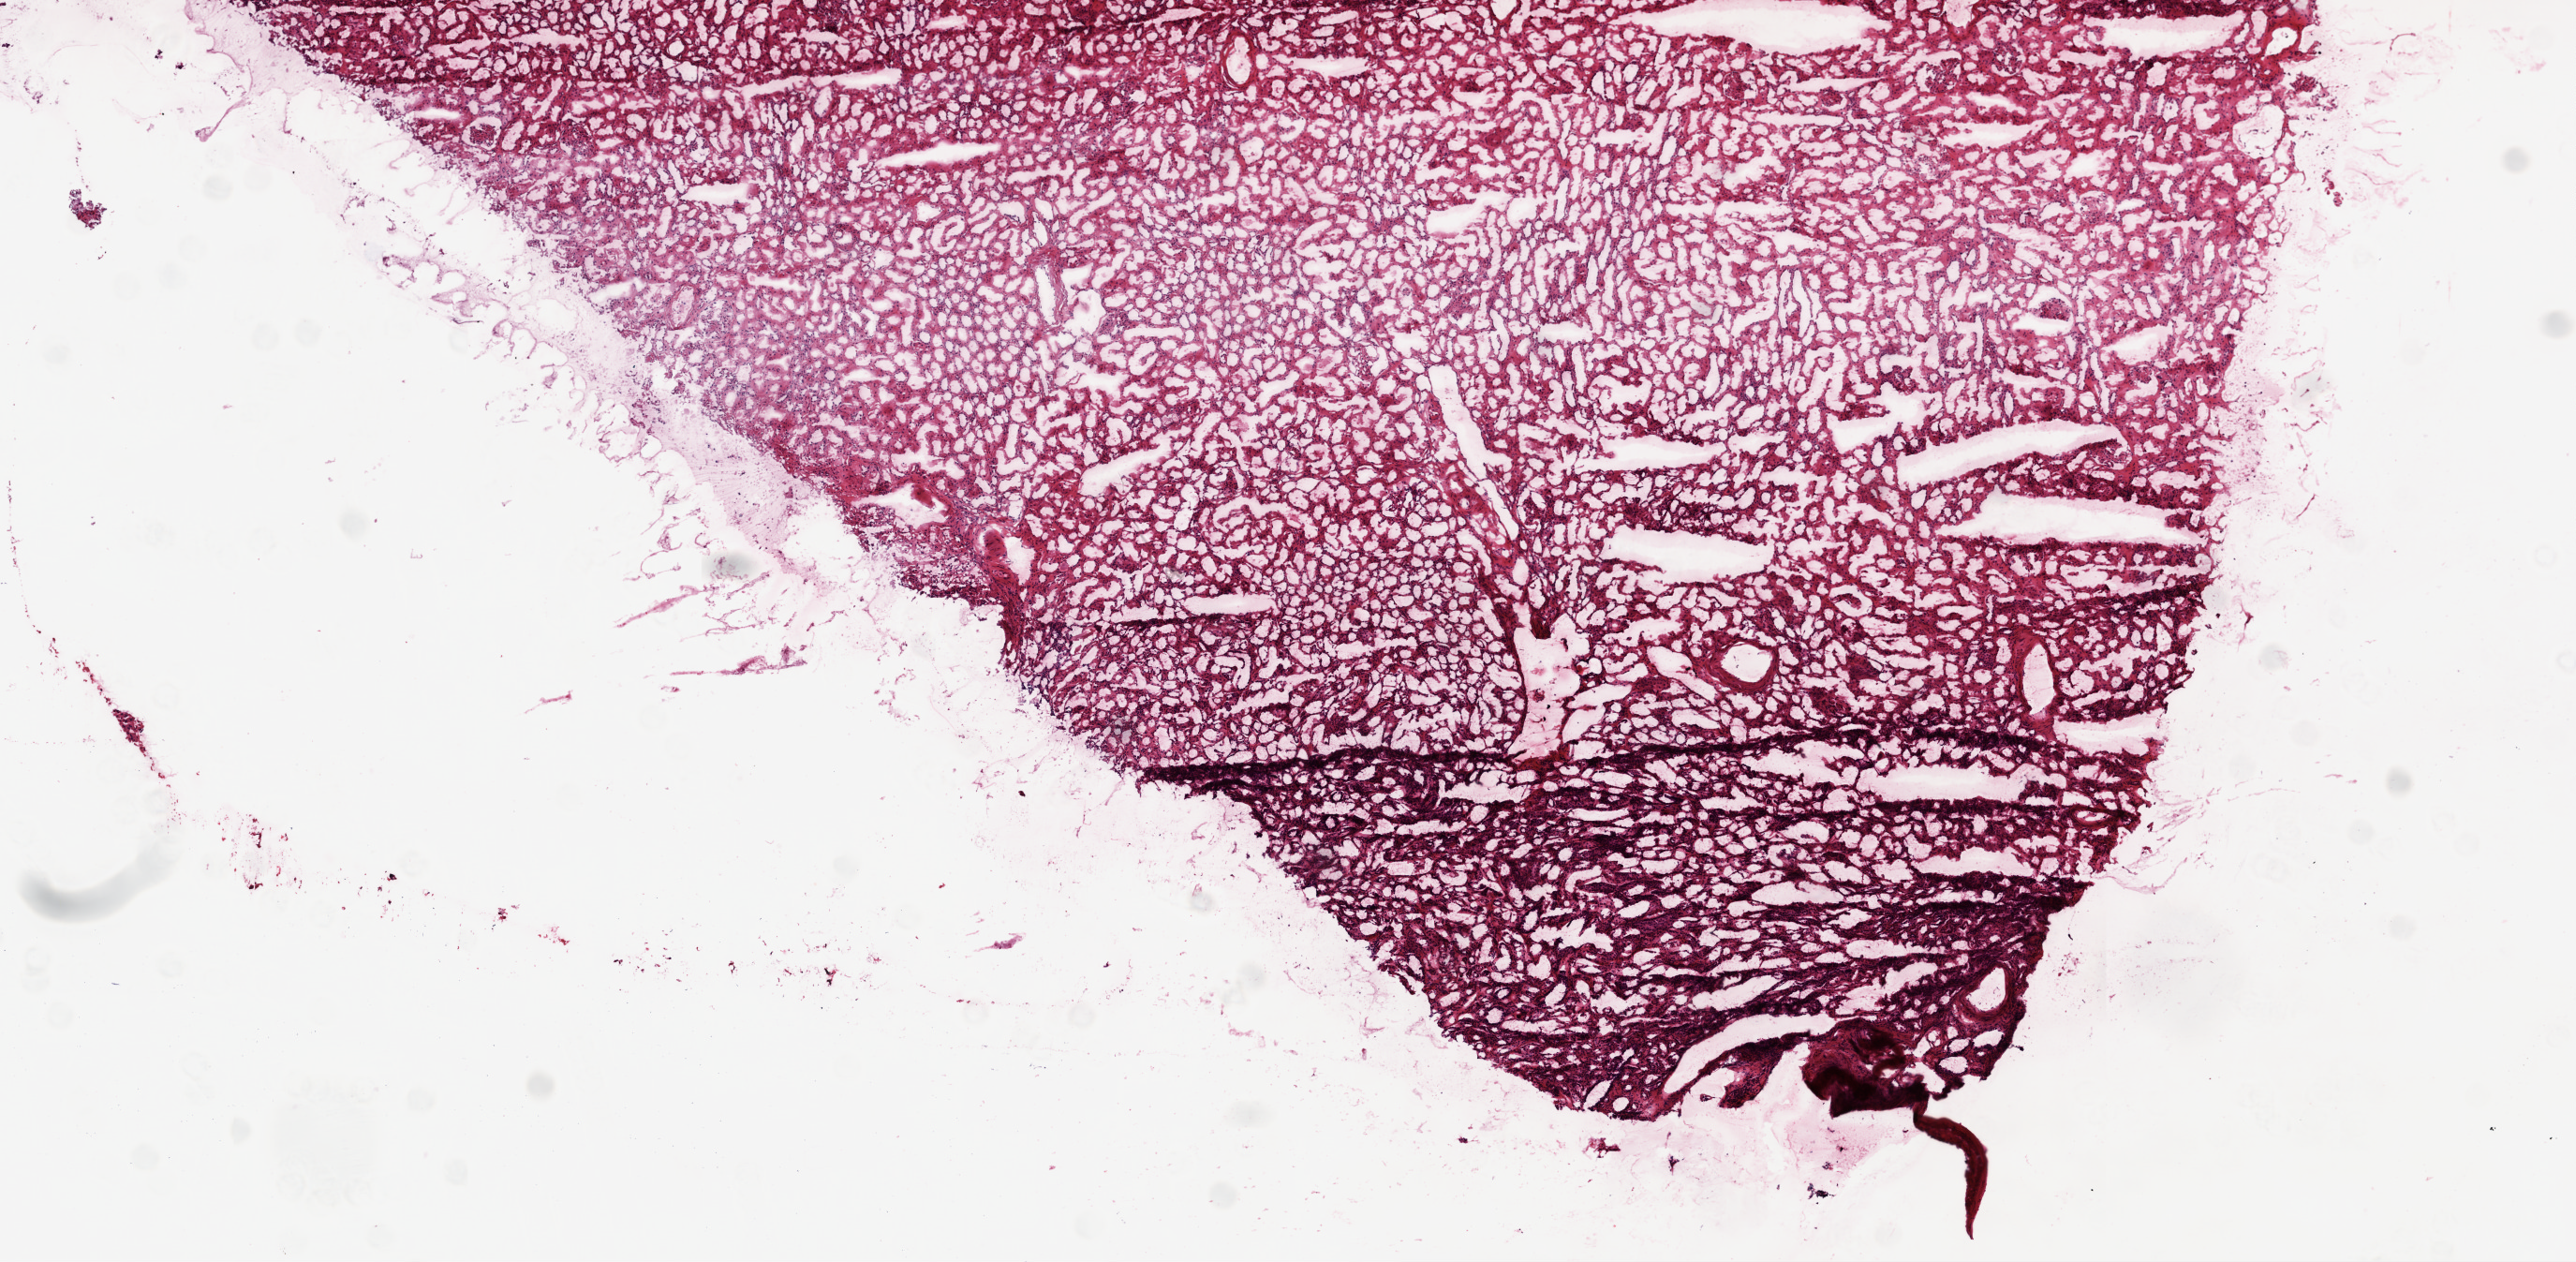
Whole-slide histology image, H&E-stained — low-resolution overview of the scanned area, about 11.0 x 5.4 mm (slide scanned at 20x). Frozen section from the top of the tissue portion. Solid tissue normal (non-tumour tissue) sample from the kidney. Patient: female, age at initial diagnosis 82 years.
This section: solid tissue normal sample (biorepository sample class). Patient diagnosis: Clear cell adenocarcinoma, NOS.